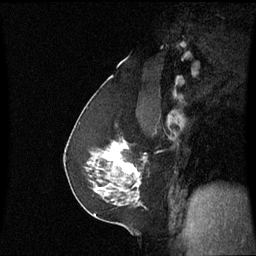
Breast MRI (dynamic contrast-enhanced), one sagittal slice. Slice 38 of 60 in the series (ordered by position). Dynamic contrast-enhanced series, image 2 of 3 at this slice position (ordered by acquisition). 1.5 T. TE 4.2 ms, TR 8.9 ms. 2.2 mm slice thickness. 256 × 256 image matrix. Patient: female, 58 years. Case-level facts recorded for this patient, not image findings: setting: breast cancer imaged before/during neoadjuvant chemotherapy; receptor status: triple-negative.
Structures marked on this image (semi-automatic segmentation, software-assisted and operator-edited):
- analysis volume of interest (the breast-tissue region the enhancement analysis was run in; not a lesion): bounding box (x1, y1, x2, y2) in pixels: (90, 140, 147, 193)
- tumour enhancement mask (voxels above the 70 % enhancement threshold inside the analysis volume of interest): (104, 142, 139, 187)